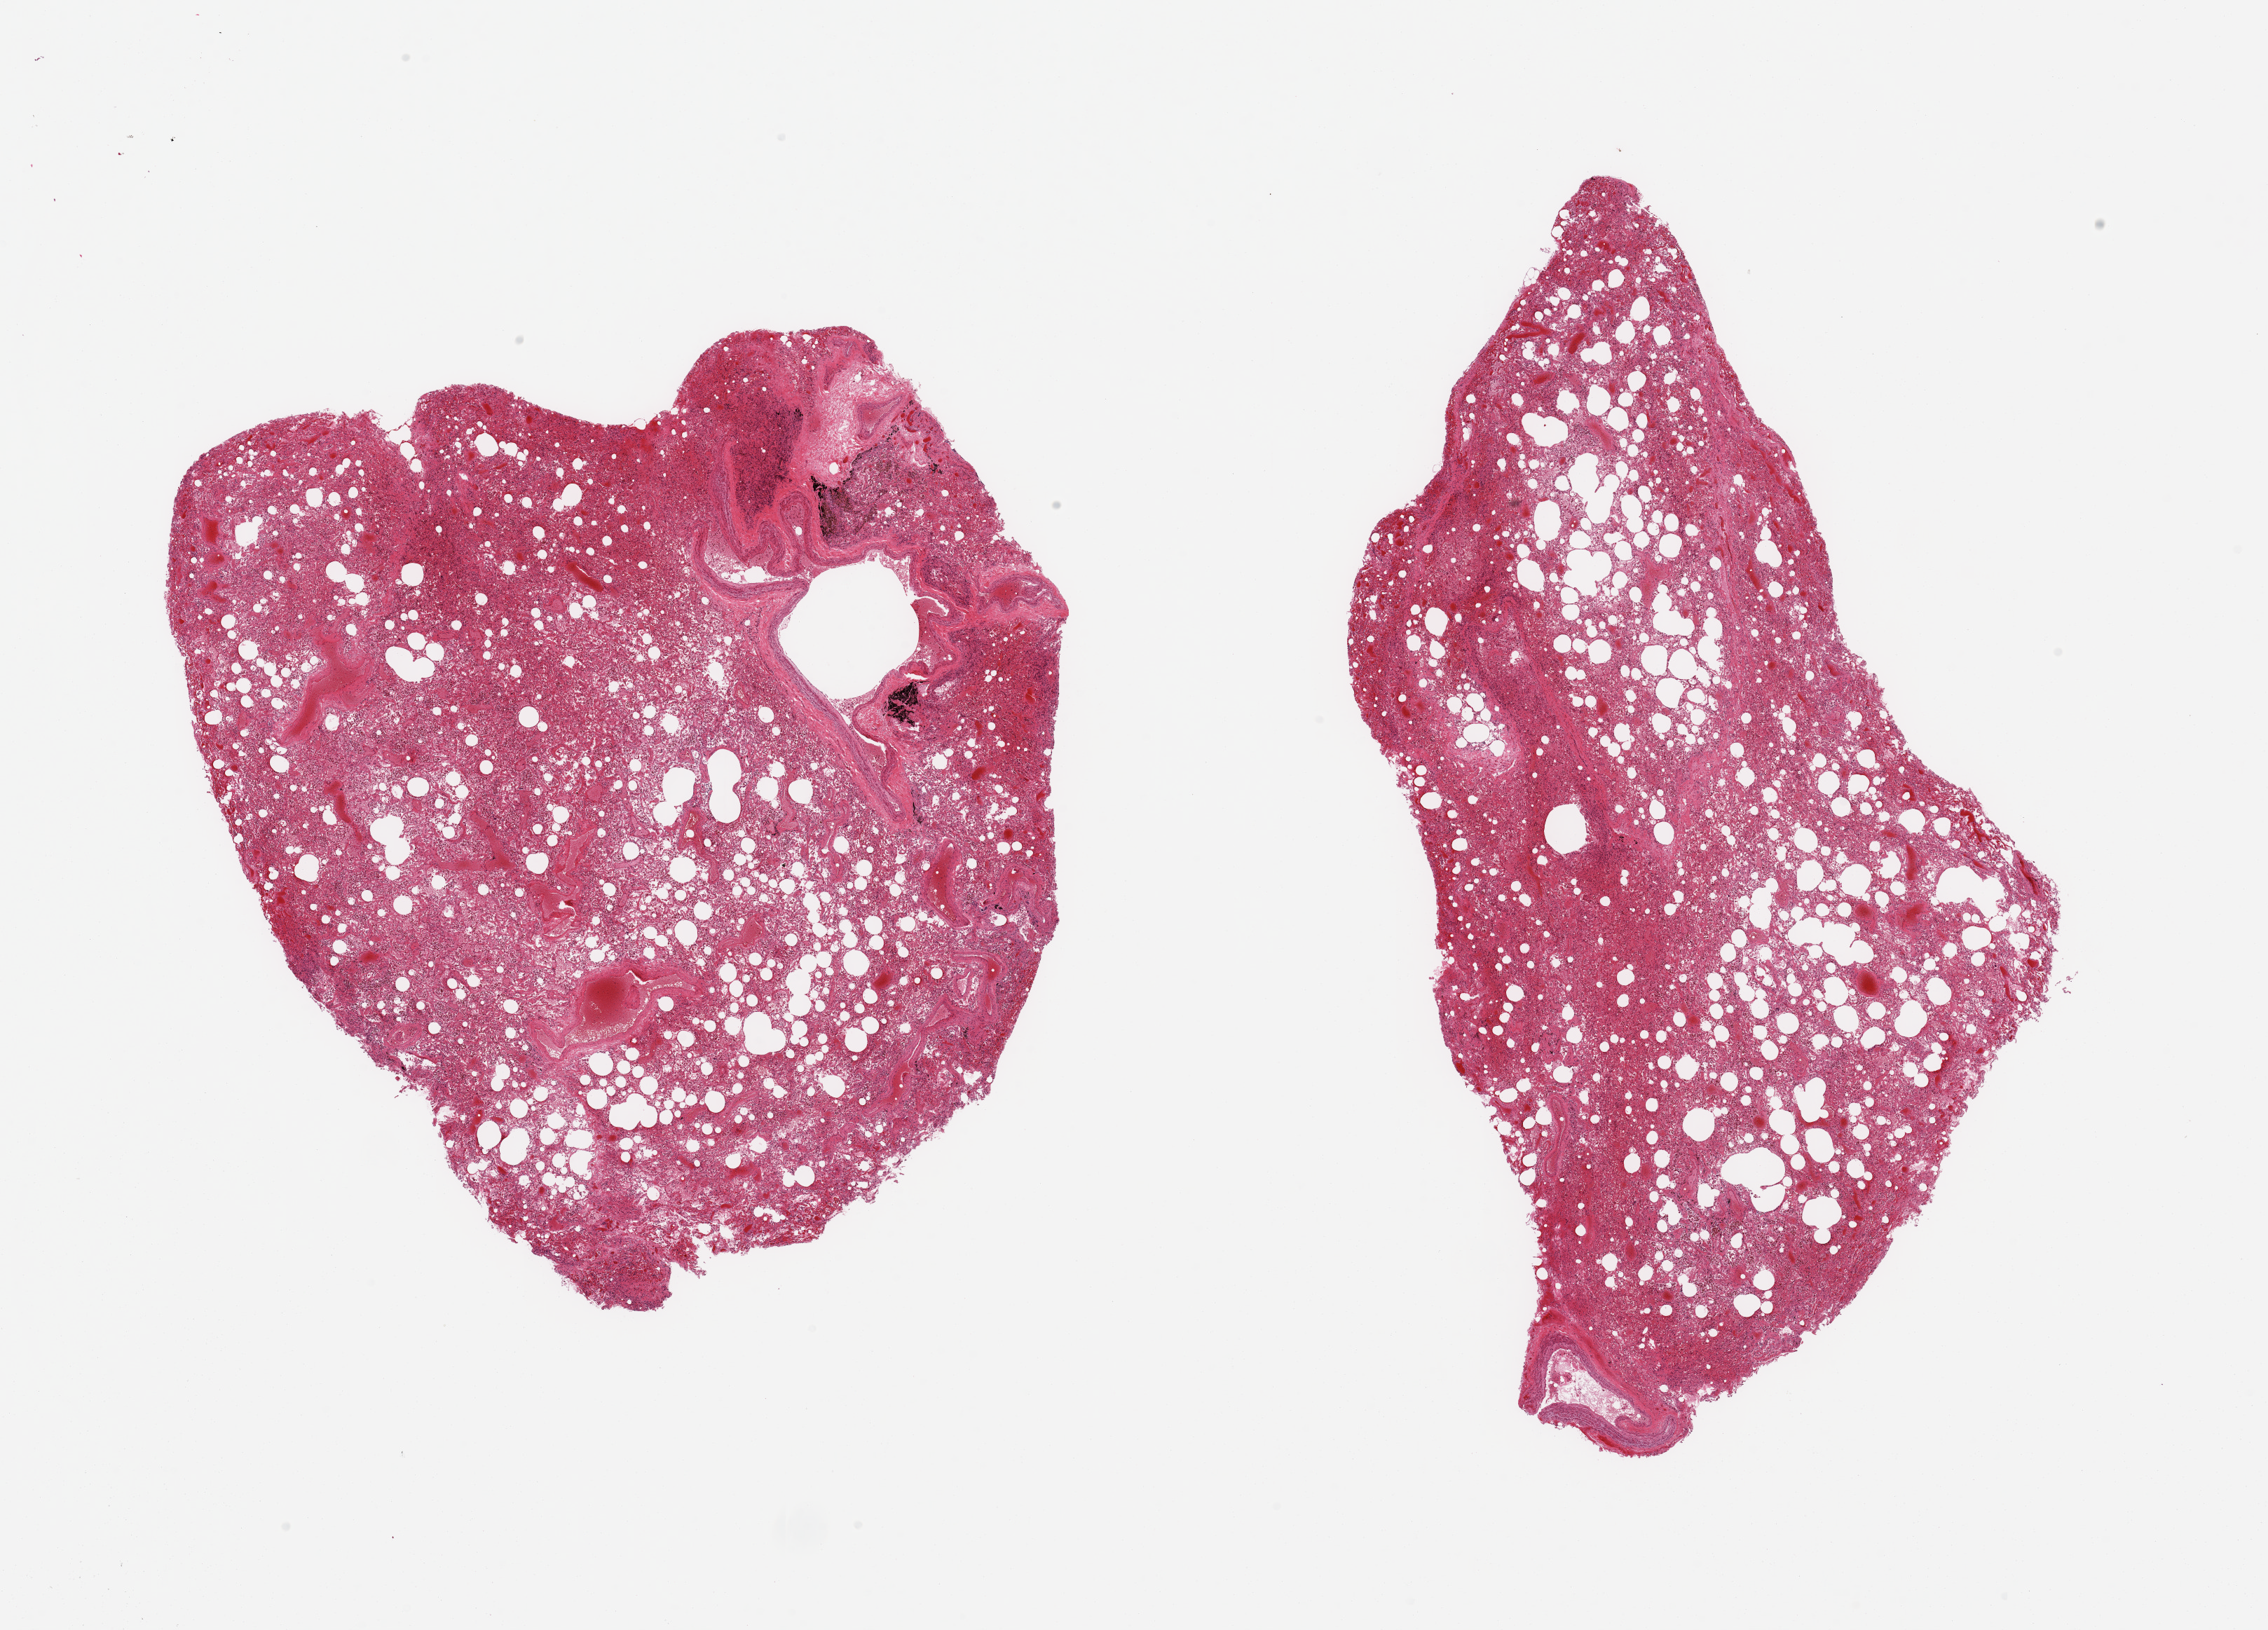
Whole-slide image, H&E stain, brightfield — a low-resolution overview of the entire scanned area, about 25.6 x 18.4 mm (acquisition: 20x scan), PAXgene-fixed, paraffin-embedded tissue, section of lung (target tissue), tissue donor sample. Male donor.
- review note (as recorded): 2 pieces; marked congestion and hemosiderosis; anthracosis; large and irregular in shape empty spaces bounded by congested capillaries; larger vessels included